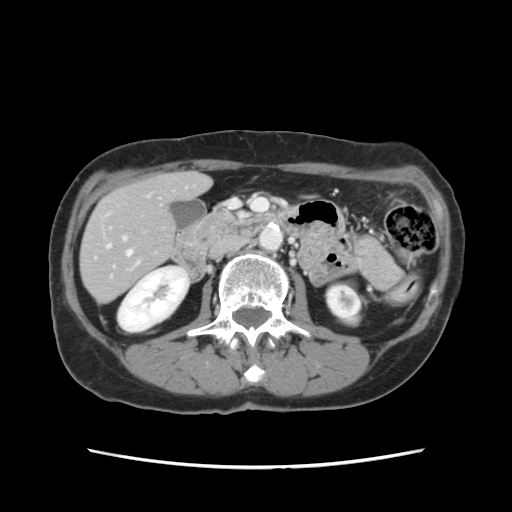
Contrast-enhanced abdominal CT, one axial slice. Slice 42 of 120 in the series (ordered by position). 120 kVp. Intravenous contrast given. Soft-tissue window (W 400 / L 40 HU). 512 × 512 image matrix, field of view 330 × 330 mm. Female patient, age 70 years. Case-level facts recorded for this patient, not image findings: diagnosis: colorectal cancer liver metastases, imaged before liver resection; multiple liver metastases: no; largest metastasis: 2.5 cm; disease in both lobes: no.
Outlined on this slice (outlined manually by an expert reader):
- hepatic veins: box from (x=107, y=244) to (x=132, y=256) px
- liver: (x=81, y=173)–(x=209, y=301)
- planned liver remnant (the part of the liver to remain after resection): (x=81, y=173)–(x=208, y=302)
- portal vein (with intrahepatic branches): (x=123, y=236)–(x=126, y=240)